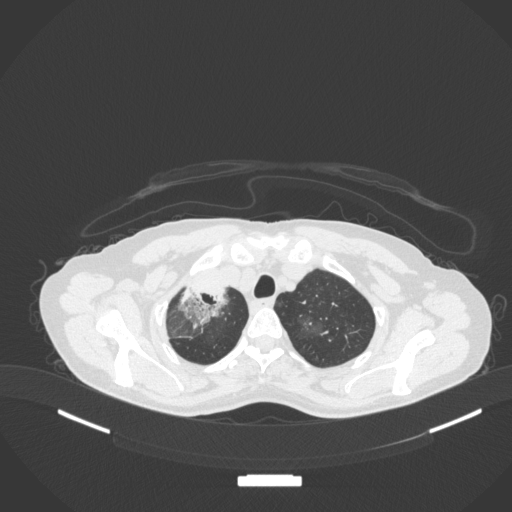
Chest CT, one axial slice. Slice 279 of 311 in the series (ordered by position). 120 kVp. Lung window (W 1500 / L -600 HU). 1 mm slice thickness. 512 × 512 image matrix. Female patient, age 59 years. Case-level facts recorded for this patient, not image findings: clinical TNM (as recorded): T3 N0 M0; histopathological grade: G1.
Structures marked on this image (bounding box drawn by a radiologist):
- lung tumour (recorded histology: adenocarcinoma): box from (x=179, y=282) to (x=231, y=331) px